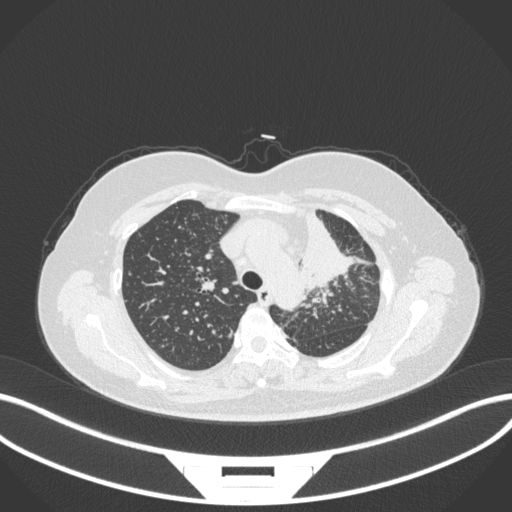
Chest CT, one axial slice. Slice 252 of 348 in the series (ordered by position). Reconstruction kernel B31f. 120 kVp. Lung window (W 1500 / L -600 HU). 512 × 512 image matrix, field of view 400 × 400 mm. Patient: female, 49 years. Case-level facts recorded for this patient, not image findings: clinical TNM (as recorded): T1c N0 M1.
Annotated regions visible in this slice (bounding box drawn by a radiologist):
- lung tumour (recorded histology: adenocarcinoma): box from (x=299, y=206) to (x=358, y=292) px